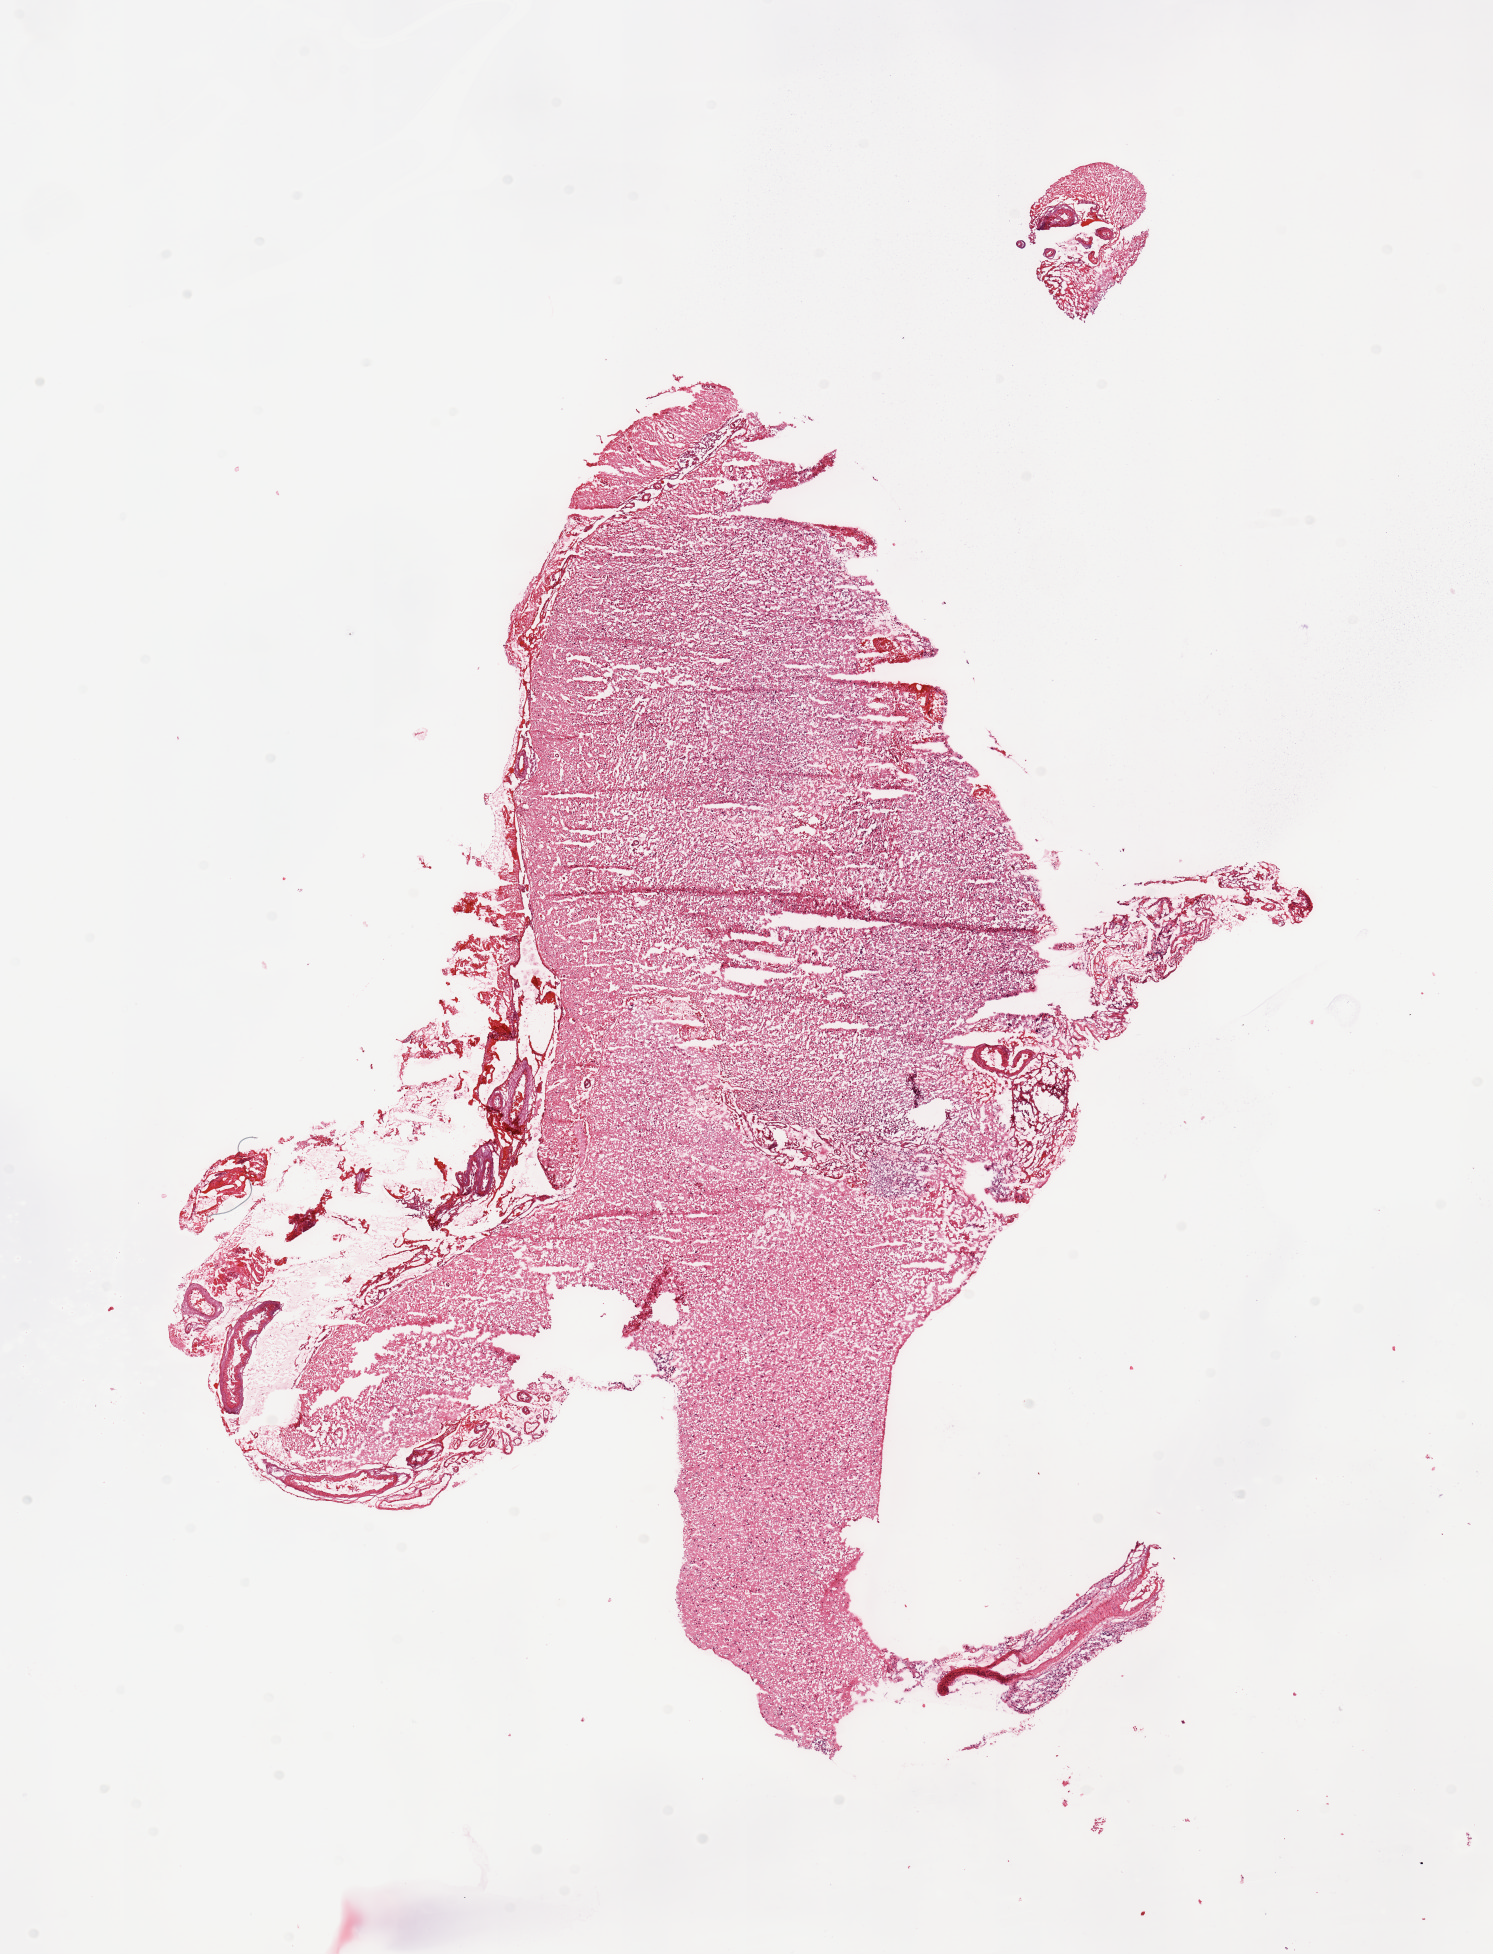
Whole-slide histology image, Hematoxylin and eosin (H&E) stained — shown as a low-resolution overview of the whole scanned area (about 11.8 x 15.5 mm, slide scanned at 20x). Brain, tumour tissue. 60-year-old male patient.
Primary tumour site (as recorded): parietal lobe. Patient diagnosis (cohort enrolment): glioblastoma multiforme (brain).